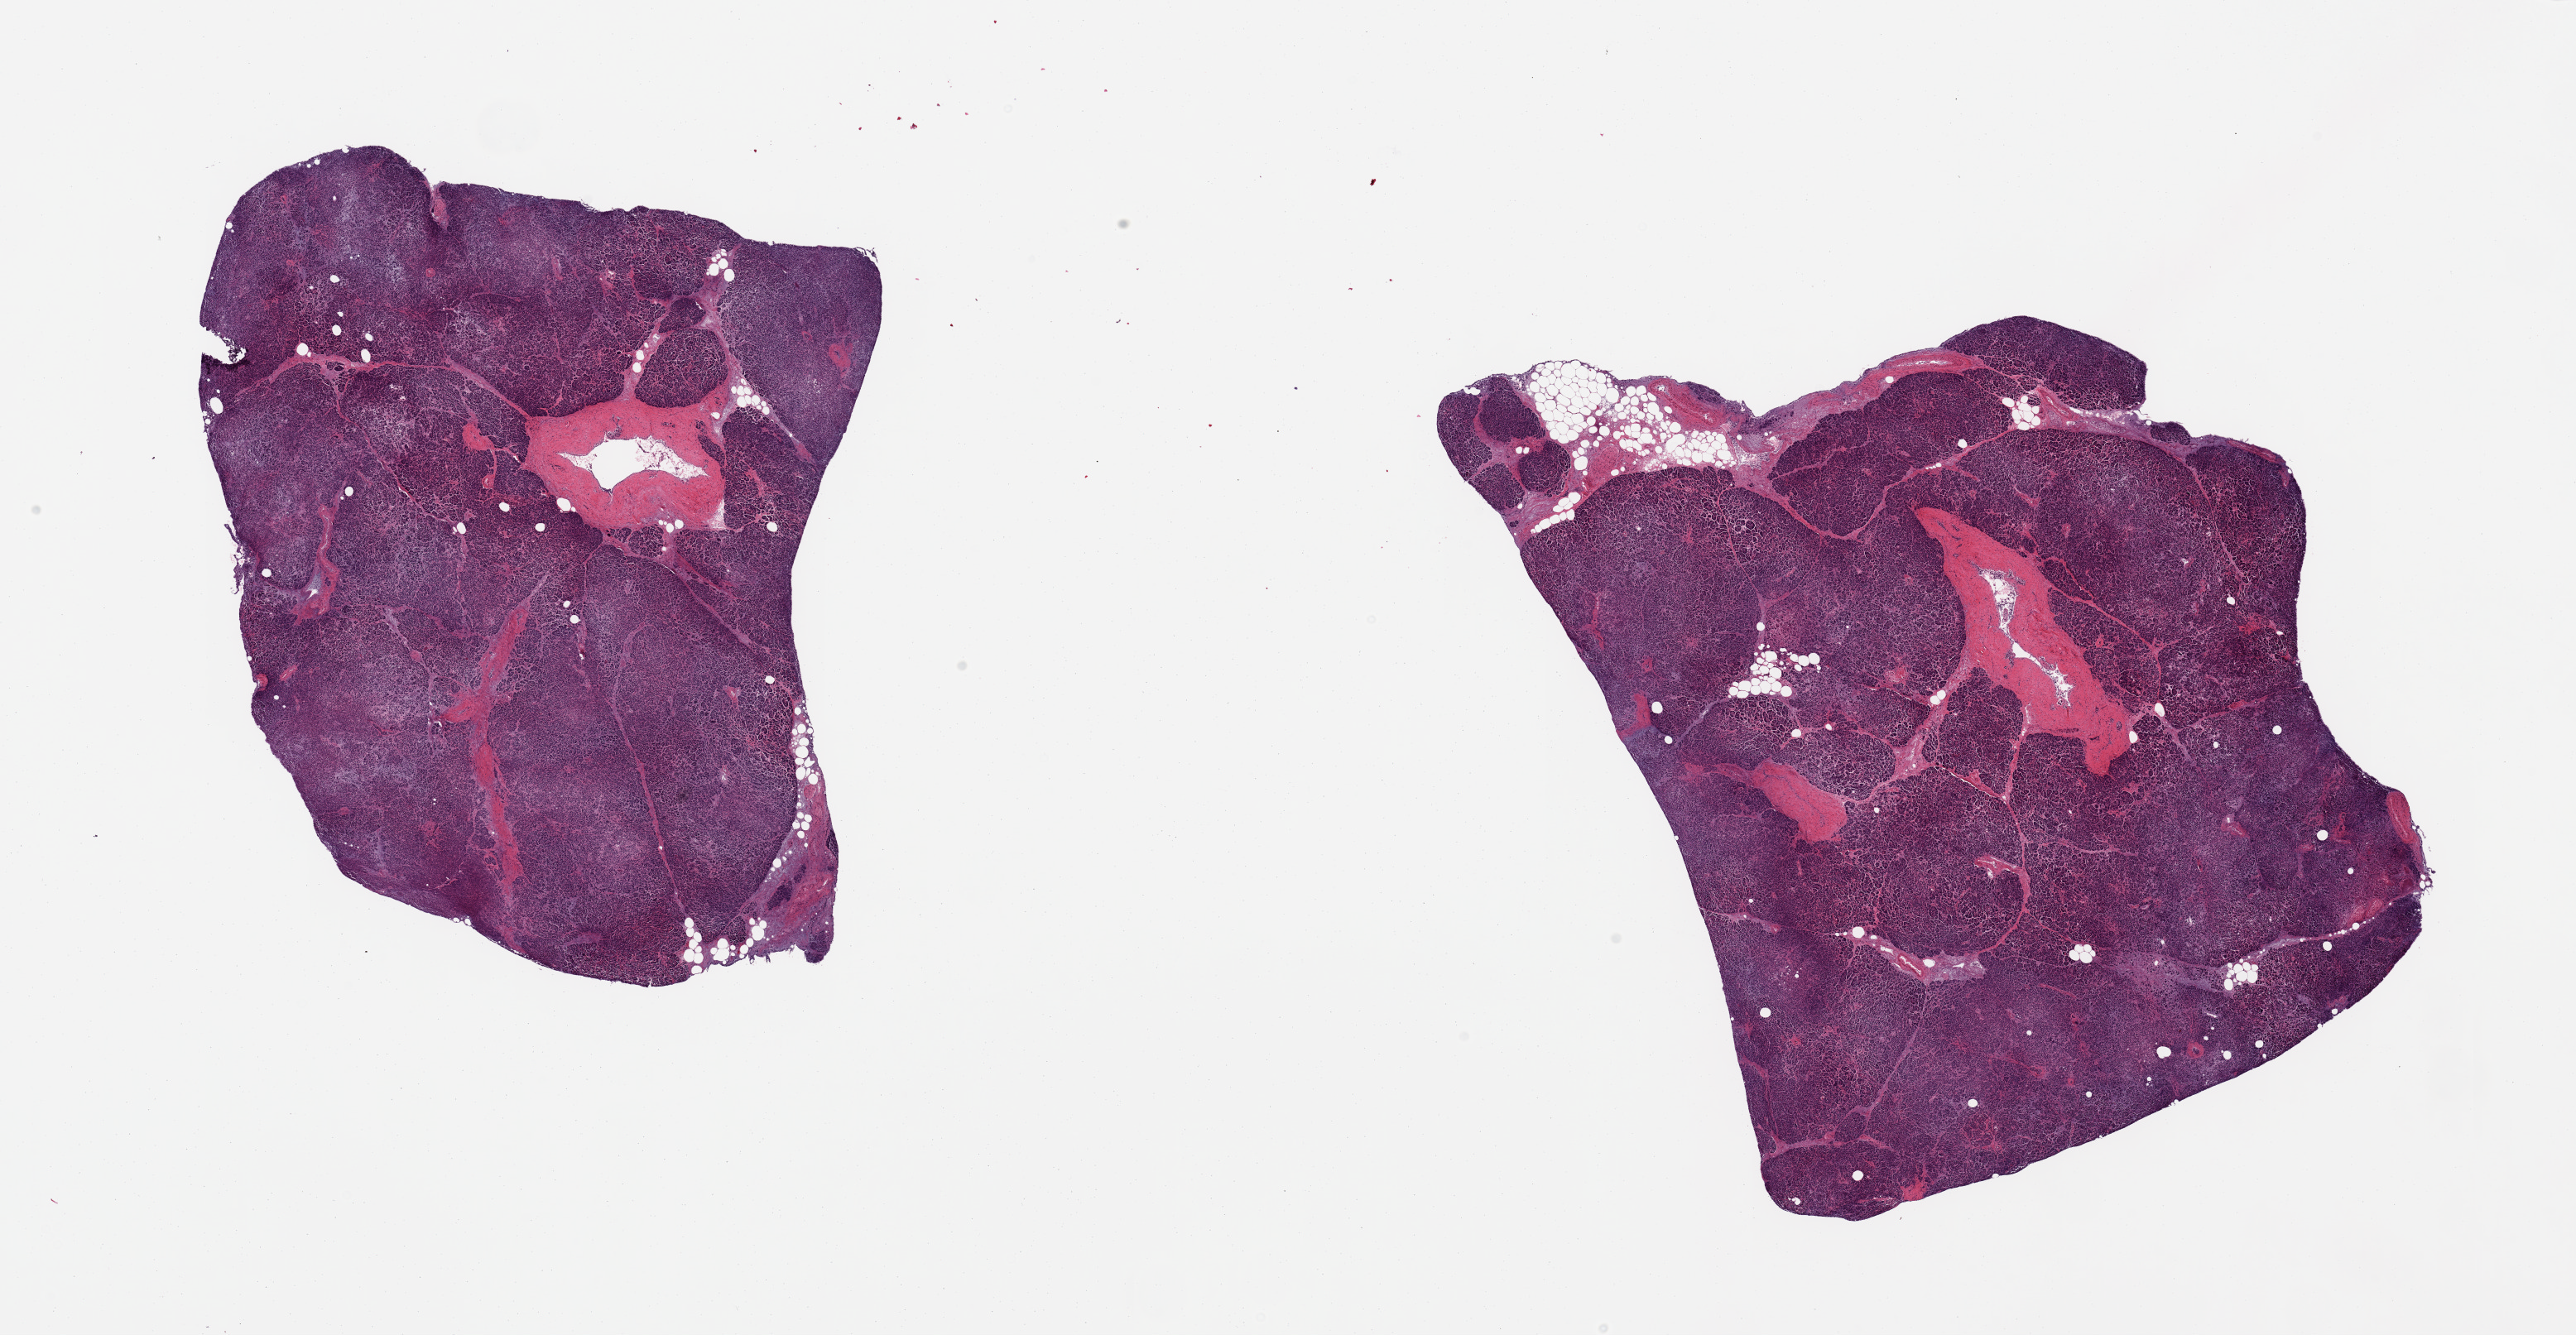
Digitized hematoxylin and eosin (H&E)-stained section — low-resolution overview of the scanned area, about 24.6 x 12.8 mm; PAXgene-fixed paraffin-embedded (PFPE) section; sampled site (target tissue): pancreas; tissue donor sample. Donor: male.
Pathologist's review note for this sample: 2 pieces, moderately advanced saponification, Islets no well preserved.